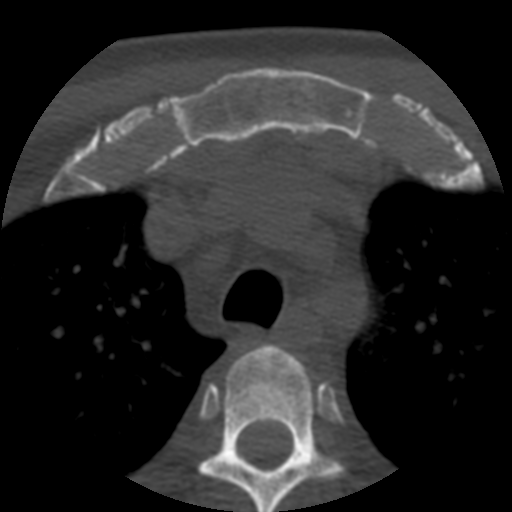
CT including the spine, one axial slice; position 414 of 508 along the scan axis; reconstruction kernel STANDARD; bone window (W 1800 / L 400 HU); 1.25 mm slice thickness; 512 × 512 image matrix, field of view 160 × 160 mm. Patient age 57 years. From the clinical record (not read from this slice): primary cancer: prostate.
Annotated regions visible in this slice (semi-automatically segmented with operator editing):
- T3 vertebra: box from (x=199, y=345) to (x=341, y=512) px